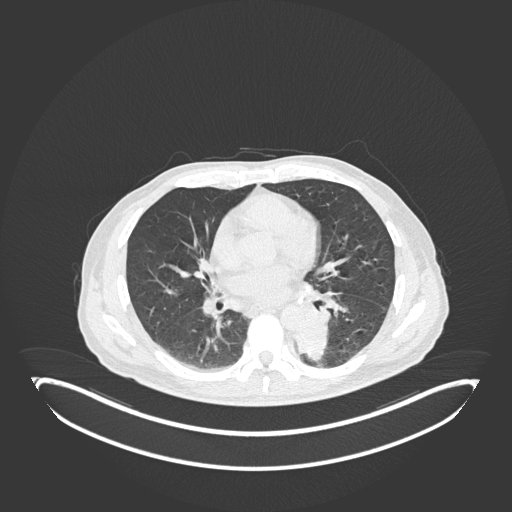
Chest CT, one axial slice; position 92 of 251 along the scan axis; 120 kVp; lung window (W 1500 / L -600 HU); 1 mm slice thickness; 512 × 512 image matrix. Male patient, age 72 years. Case-level facts recorded for this patient, not image findings: clinical TNM (as recorded): T2b N0 M1.
Structures marked on this image (bounding box drawn by a radiologist):
- lung tumour (recorded histology: adenocarcinoma): bounding box (x1, y1, x2, y2) in pixels: (290, 323, 330, 362)